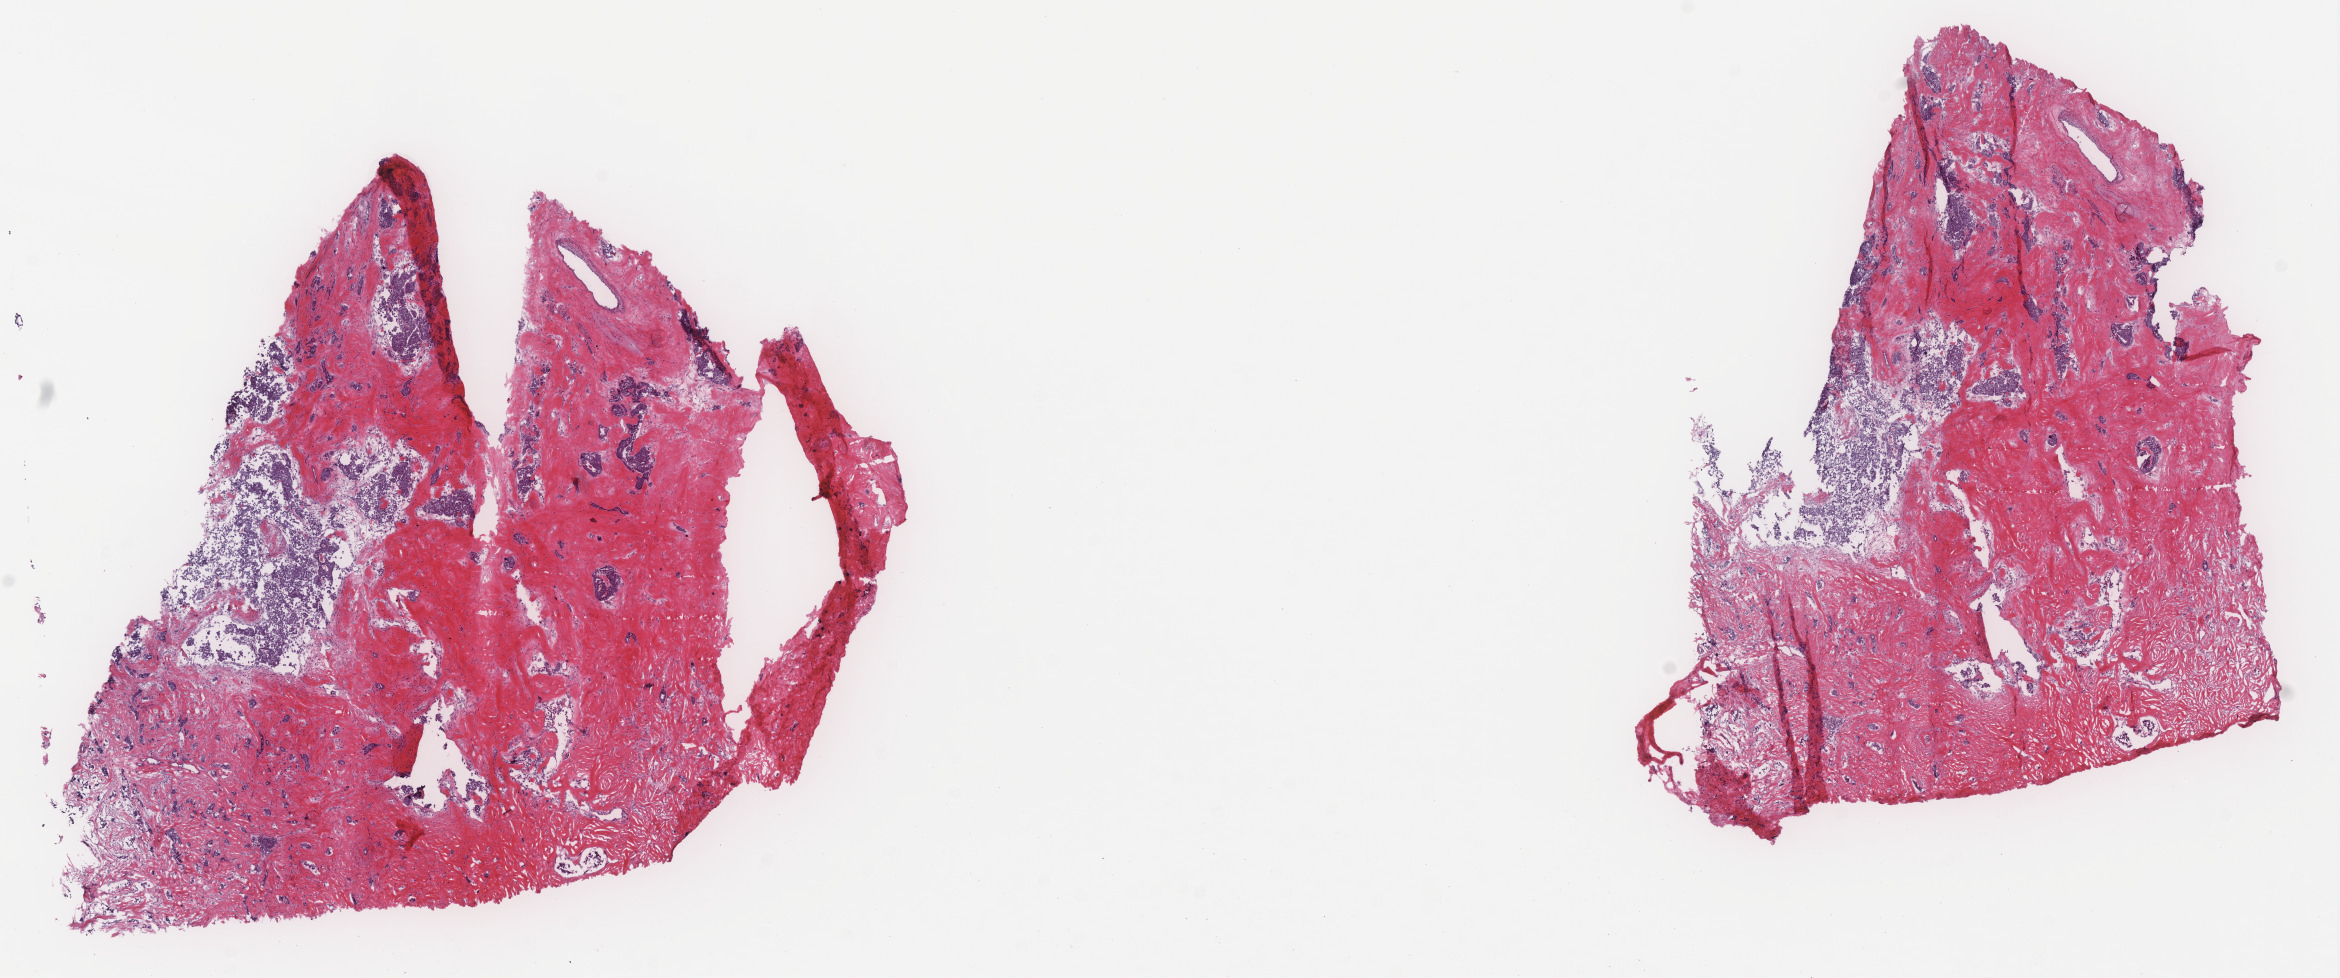
Whole-slide histology image, H&E, whole scanned area (about 18.8 x 7.8 mm, acquisition: 40x scan) shown as a low-resolution overview; frozen section from the top of the tissue portion; sample: primary tumour, breast. Female, age 69 years at initial diagnosis. Composition of this section per pathologist review: tumour cells 25%, tumour nuclei 70%, normal cells 0%, stromal cells 75%, necrosis 0%. Inflammatory infiltration, as recorded: lymphocyte infiltration 0%, monocyte infiltration 0%, neutrophil infiltration 0%.
Histologic diagnosis: Infiltrating duct carcinoma, NOS. AJCC pathologic stage: IIIA (7th edition). Lymph nodes positive (case pathology): 1 of 19 examined.